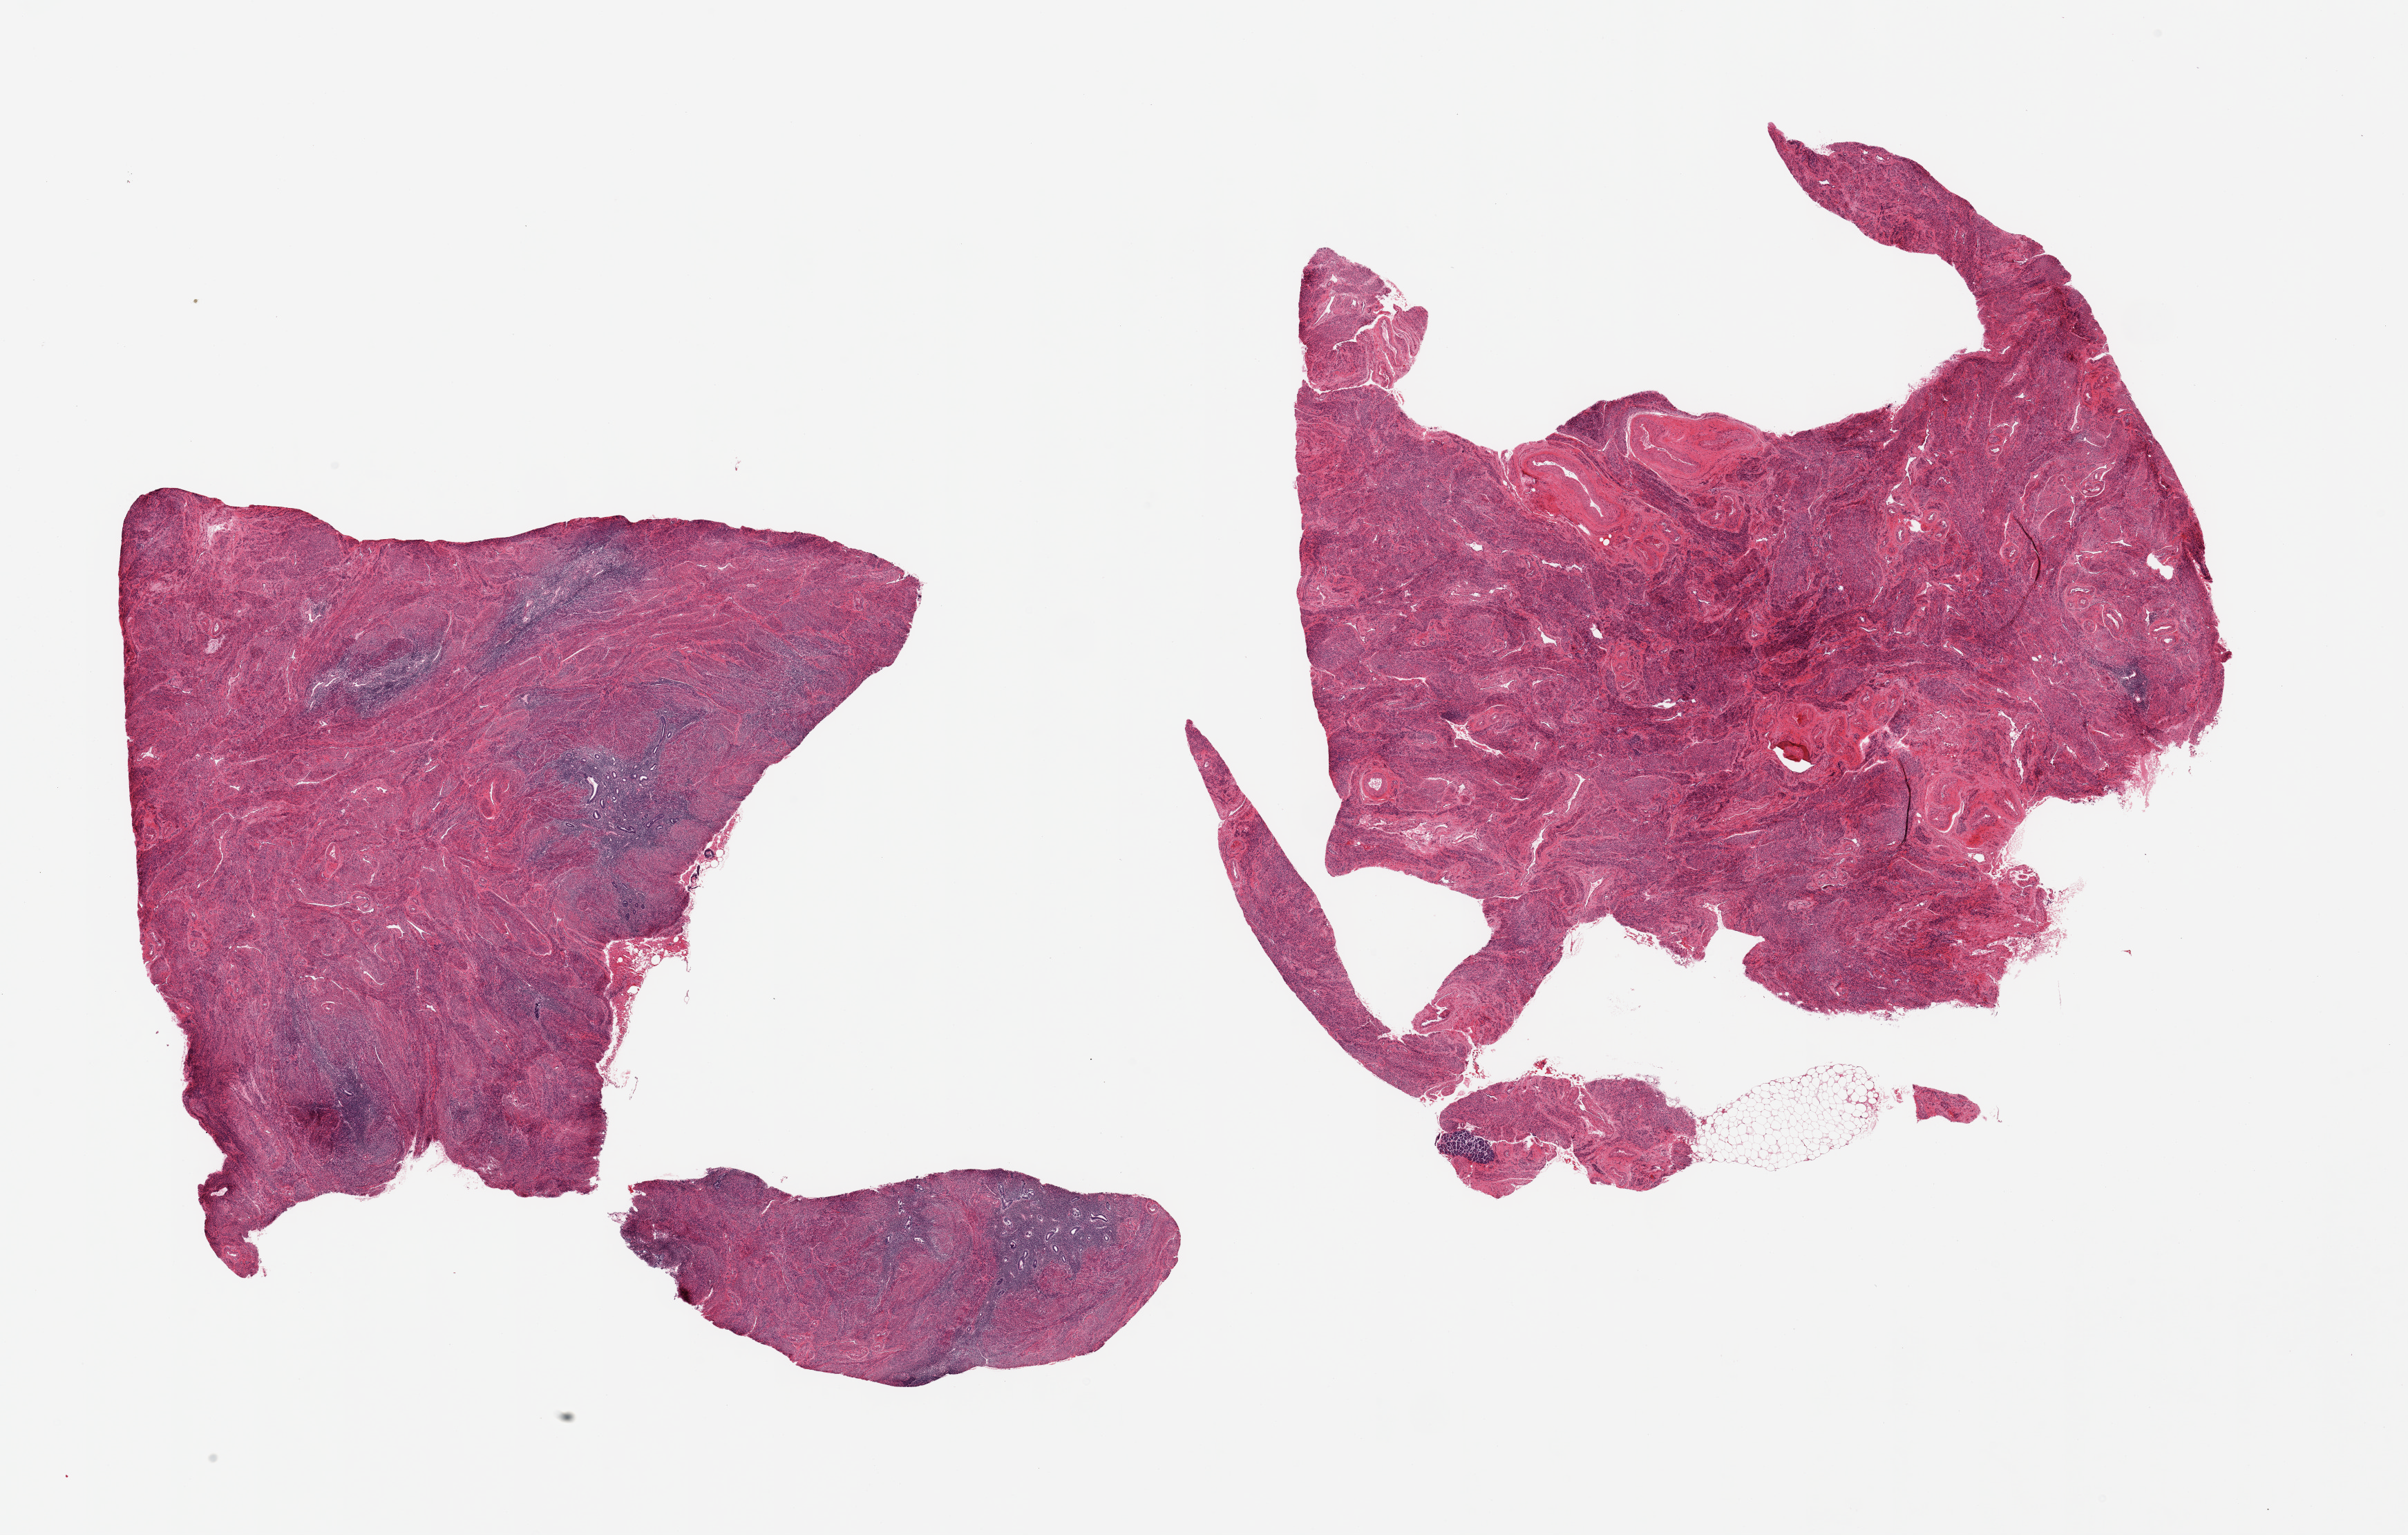
Whole-slide image, haematoxylin and eosin stain, brightfield, shown as a low-resolution overview of the whole scanned area (about 27.6 x 17.6 mm); PAXgene-fixed paraffin-embedded (PFPE) section; target tissue: uterus; donor tissue sample. Donor sex: female.
Pathologist's review note for this sample: 2 pieces; mostly myometrium withh islands of endometrium.